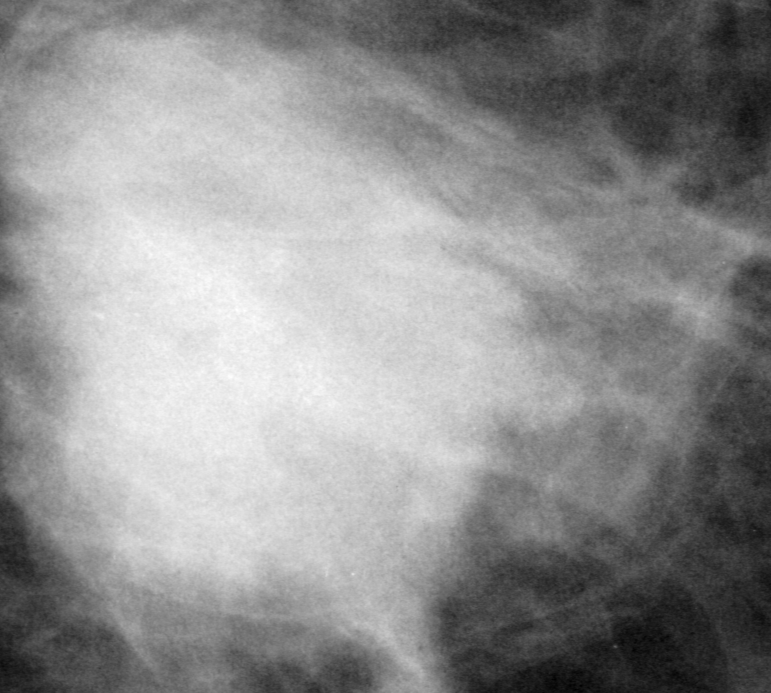
Region of interest cut from a scanned film mammogram (one marked finding); left breast; MLO view; BI-RADS breast density category 2 (scale 1–4).
Marked abnormality: mass, shape oval, margins spiculated; BI-RADS assessment category 3; subtlety rating 5 on a 1 (subtle) to 5 (obvious) scale; pathology (as recorded): malignant.